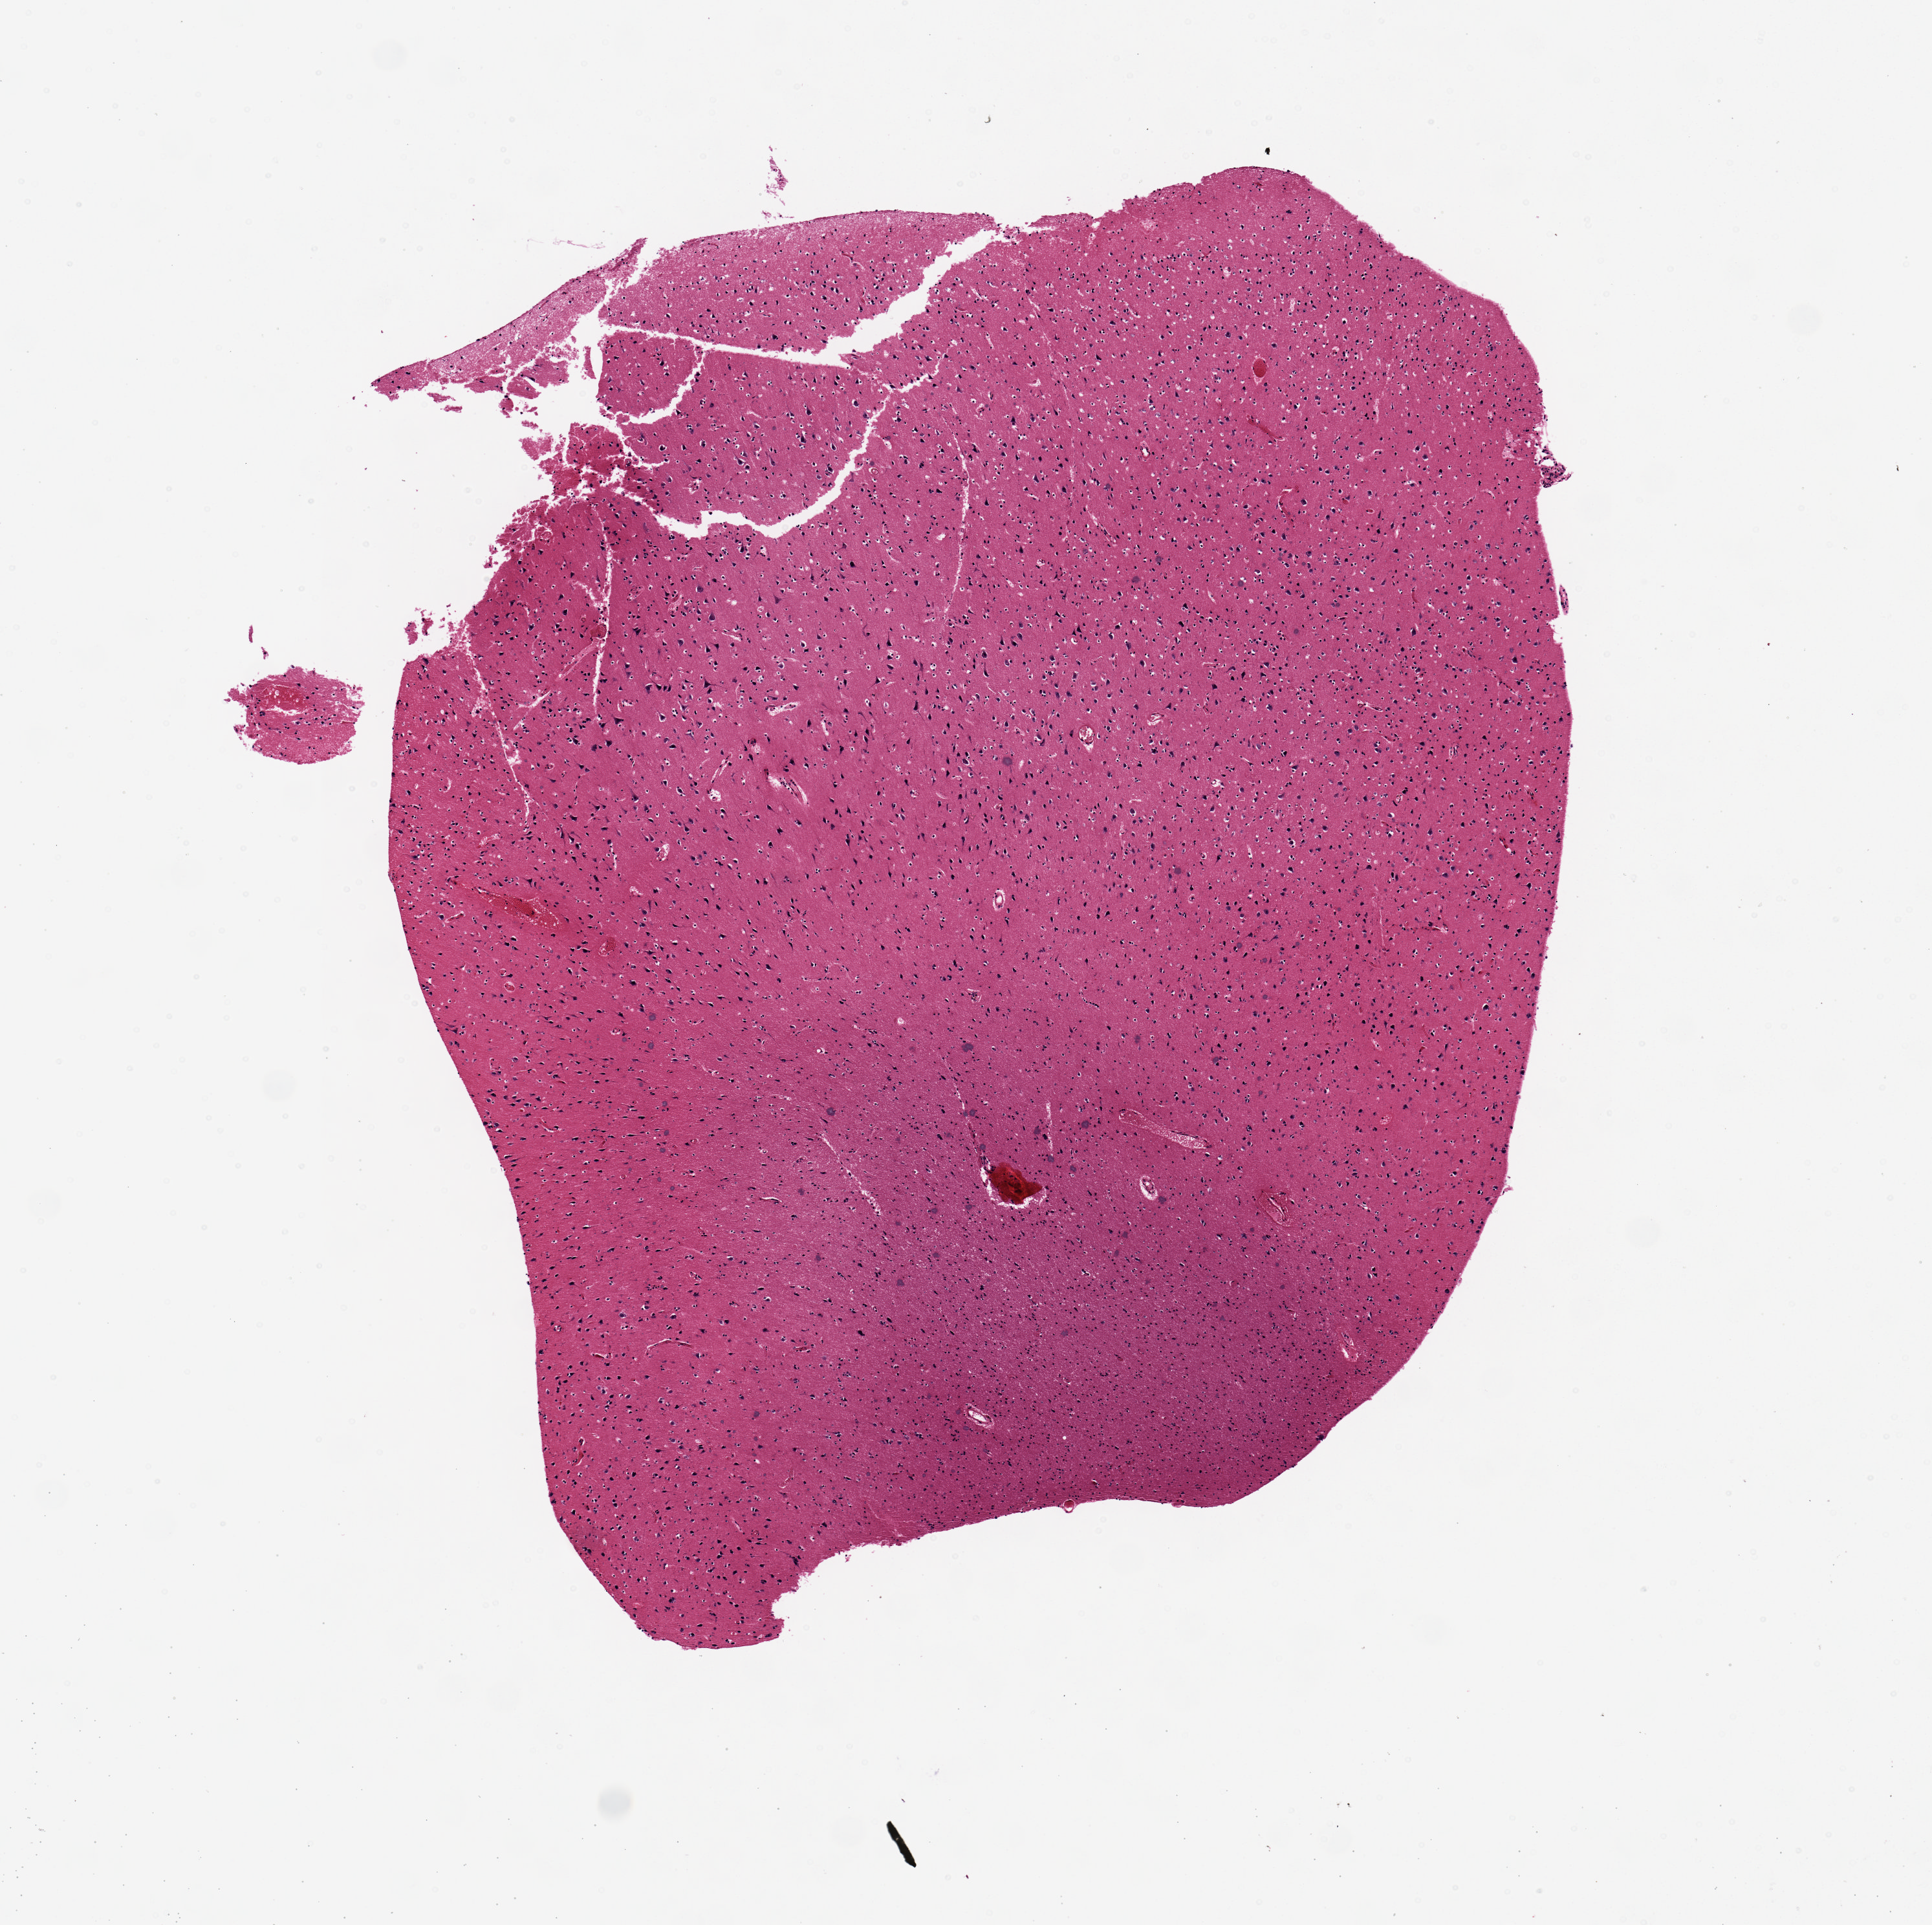
Whole-slide image, H&E stain — low-resolution overview of the scanned area, about 5.9 x 5.9 mm. PAXgene-fixed, paraffin-embedded tissue. Target tissue: cerebral cortex. Donor tissue sample. Donor: male.
Reviewer comment on this tissue sample: 5 x 3.4mm.